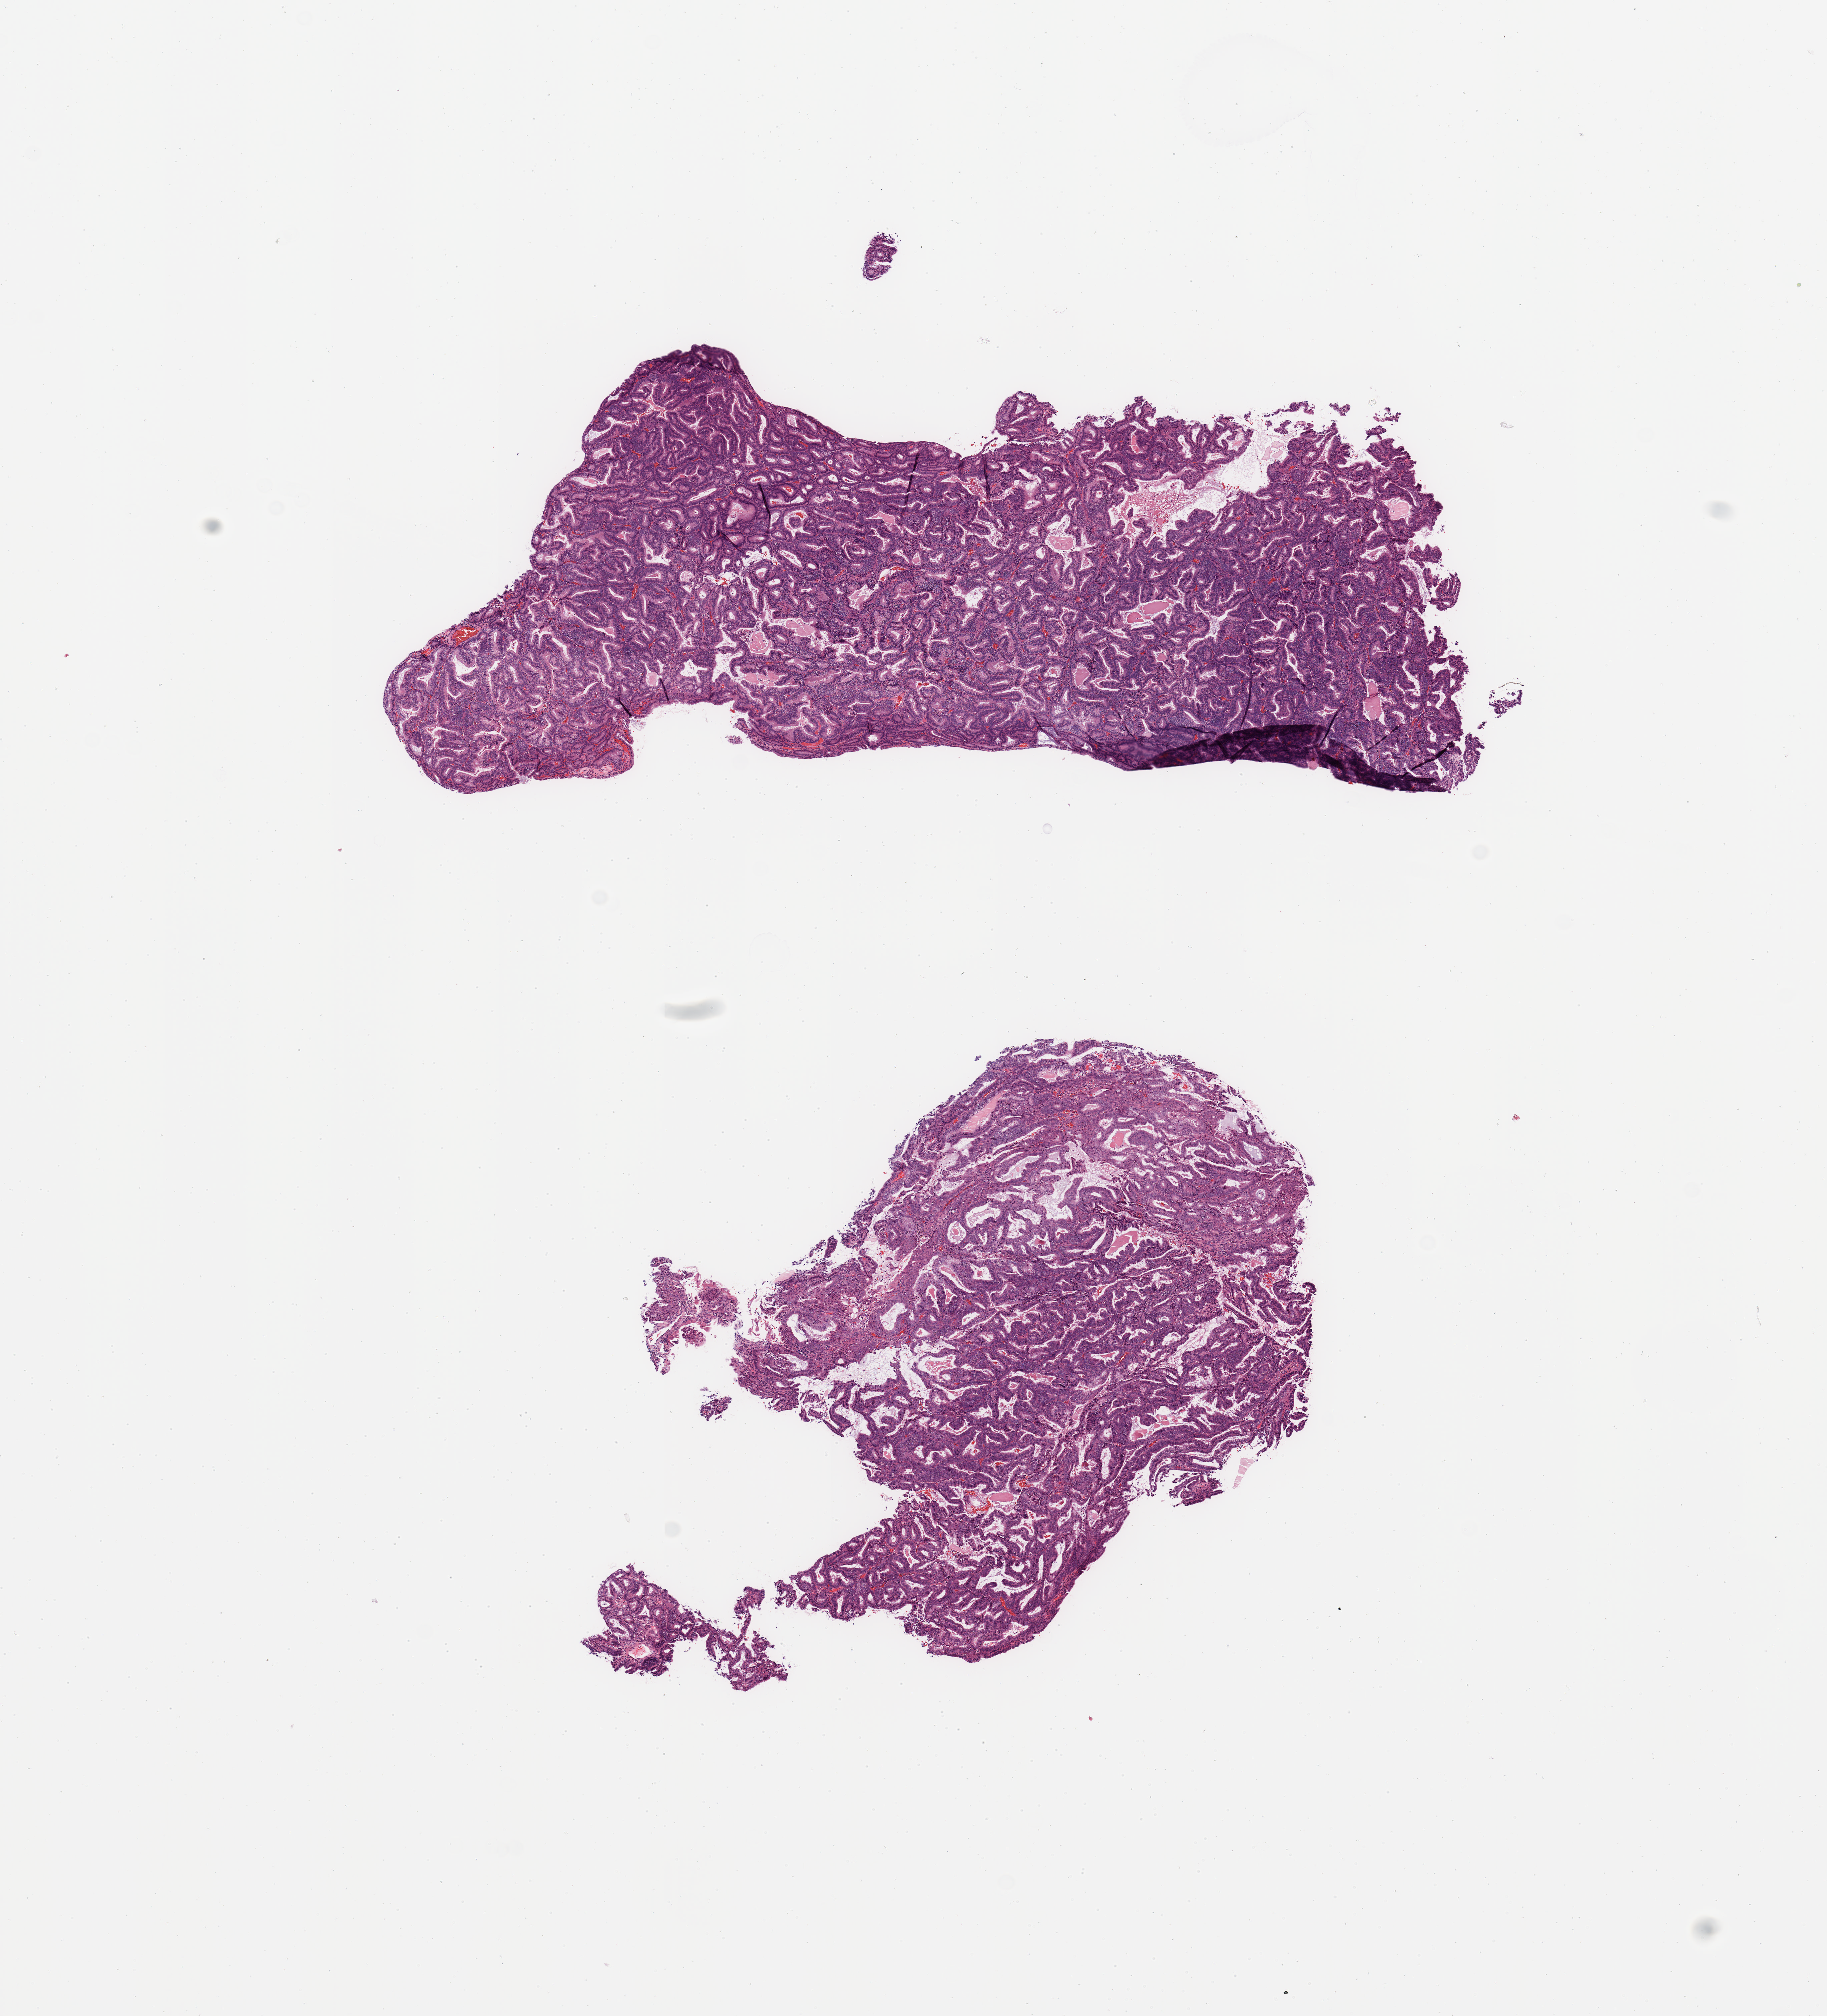
Hematoxylin and eosin (H&E) stained whole-slide image, shown as a low-resolution overview of the whole scanned area (about 10.8 x 11.9 mm, slide scanned at 20x). Uterus, tumour tissue. Female, 55 y/o. Histologic grade: G1 (well differentiated).
Histologic diagnosis: Endometrioid adenocarcinoma, NOS. AJCC pathologic stage: IV.